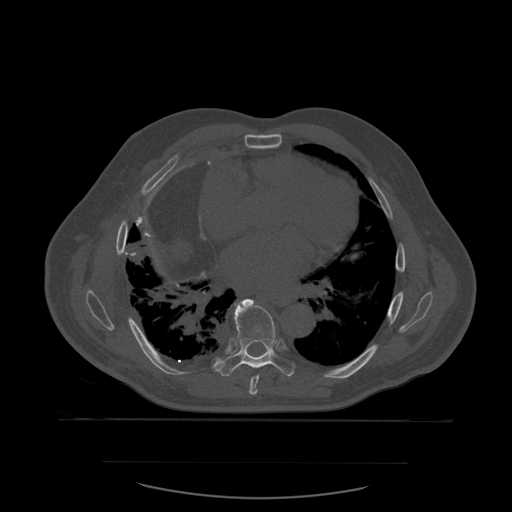
CT including the spine, one axial slice; position 366 of 590 along the scan axis; bone window (W 1800 / L 400 HU); 1.25 mm slice thickness; 512 × 512 image matrix, field of view 479 × 479 mm. Patient age 71 years. Case-level facts recorded for this patient, not image findings: primary cancer: lung; vertebrae with lytic lesions (as recorded): T1, T2, L5, S1.
Outlined on this slice (semi-automatic segmentation, software-assisted and operator-edited):
- T7 vertebra: box from (x=250, y=375) to (x=260, y=395) px
- T8 vertebra: (x=219, y=299)–(x=295, y=377)